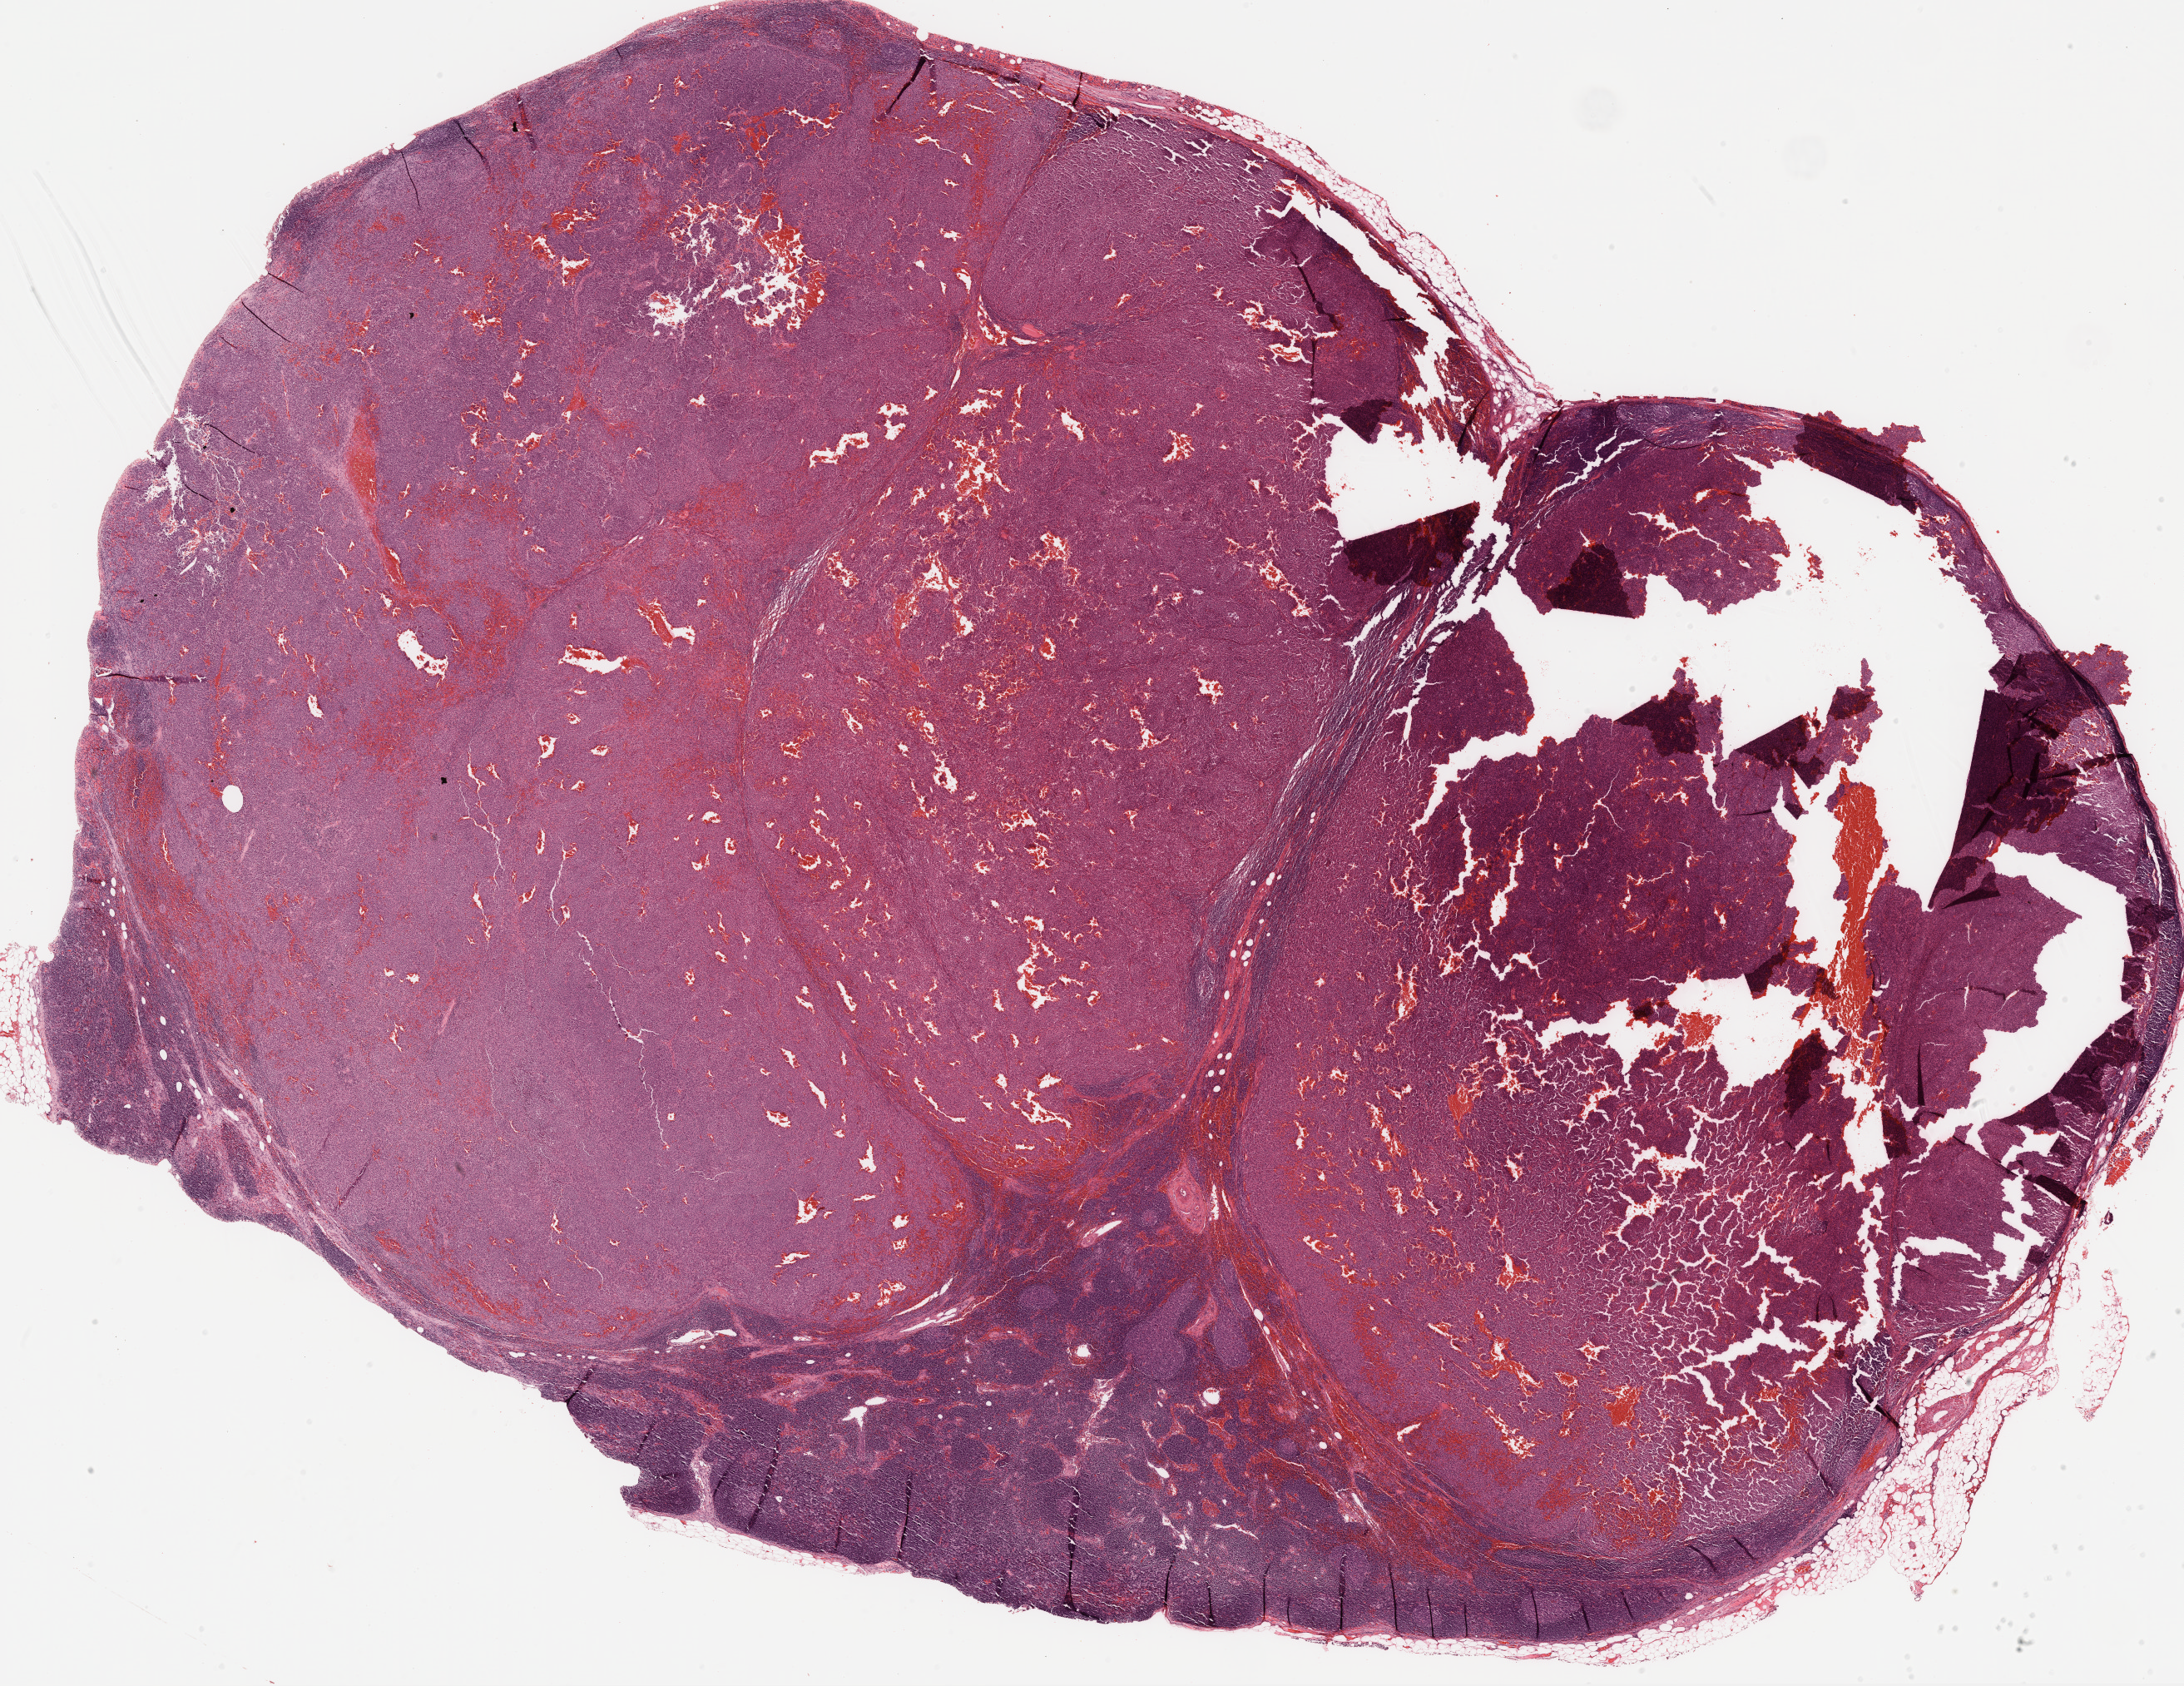
Hematoxylin and eosin (H&E) stained whole-slide image — shown as a low-resolution overview of the whole scanned area (about 21.2 x 16.3 mm, acquisition: 20x scan); FFPE section; metastatic tumour sample. Male, age 75 years at initial diagnosis.
• this section: metastatic tumour tissue
• patient diagnosis: Malignant melanoma, NOS